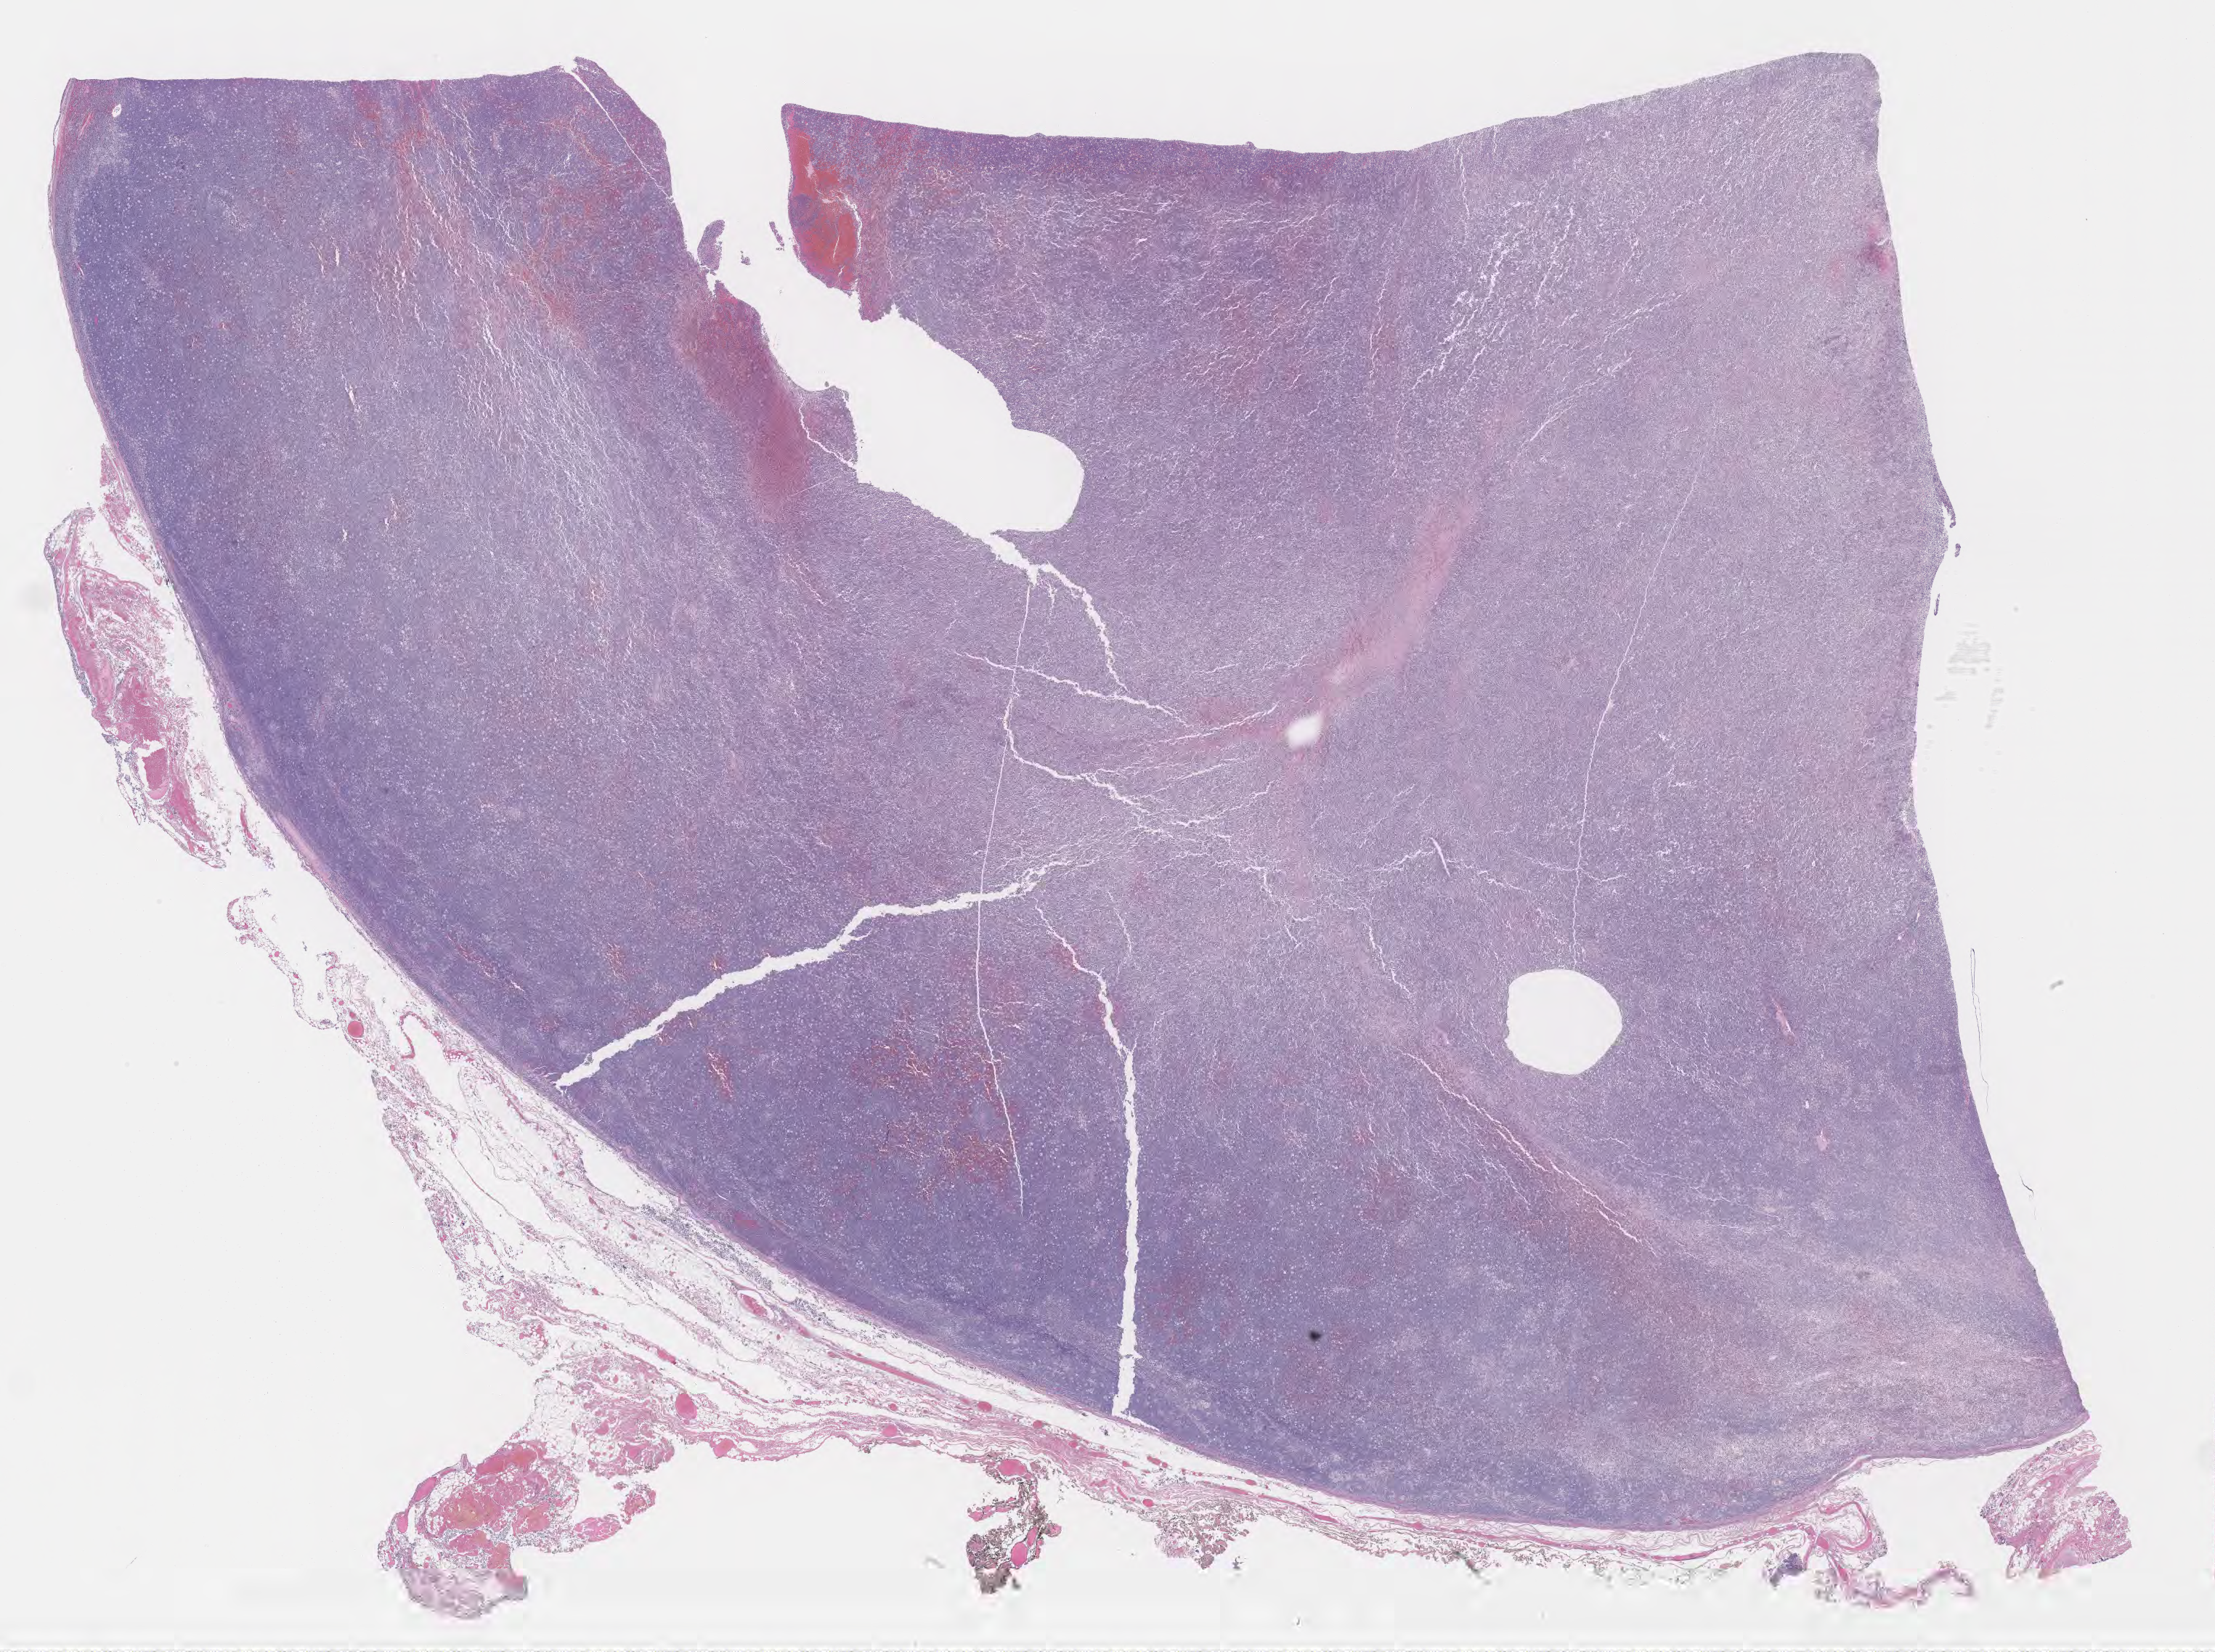
H&E whole-slide image — whole scanned area (about 24.7 x 18.4 mm) shown as a low-resolution overview, specimen: tumor tissue, site: parotid. Patient: male, aged 44.
Diagnosis: Burkitt lymphoma, NOS.